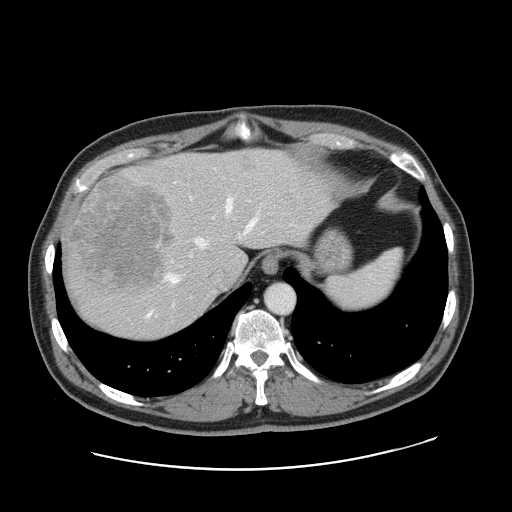
Contrast-enhanced abdominal CT, one axial slice; slice 130 of 178 in the series (ordered by position); 120 kVp; intravenous contrast given; soft-tissue window (W 400 / L 40 HU); 2.5 mm slice thickness; 512 × 512 image matrix, field of view 403 × 403 mm. Male patient, age 63 years. From the clinical record (not read from this slice): diagnosis: colorectal cancer liver metastases, imaged before liver resection.
Structures marked on this image (manually delineated by an expert):
- hepatic veins: box from (x=147, y=199) to (x=255, y=317) px
- liver: (x=64, y=149)–(x=327, y=340)
- planned liver remnant (the part of the liver to remain after resection): (x=155, y=152)–(x=327, y=278)
- portal vein (with intrahepatic branches): (x=157, y=217)–(x=214, y=246)
- liver metastasis: (x=243, y=162)–(x=255, y=170)
- liver metastasis: (x=71, y=181)–(x=175, y=288)